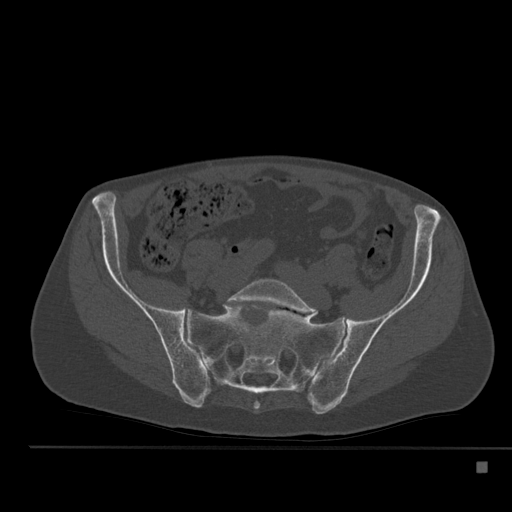
CT including the spine, one axial slice. Position 105 of 517 along the scan axis. Reconstruction kernel Br40s. 120 kVp. Bone window (W 1800 / L 400 HU). 1.5 mm slice thickness. 512 × 512 image matrix, field of view 408 × 408 mm. Male patient, age 70 years. Case-level facts recorded for this patient, not image findings: primary cancer: renal; vertebrae with lytic lesions (as recorded): T4, T6, T10, T12, L3, L4, L5.
Structures marked on this image (semi-automatic segmentation, software-assisted and operator-edited):
- L5 vertebra: bounding box (x1, y1, x2, y2) in pixels: (226, 278, 317, 316)